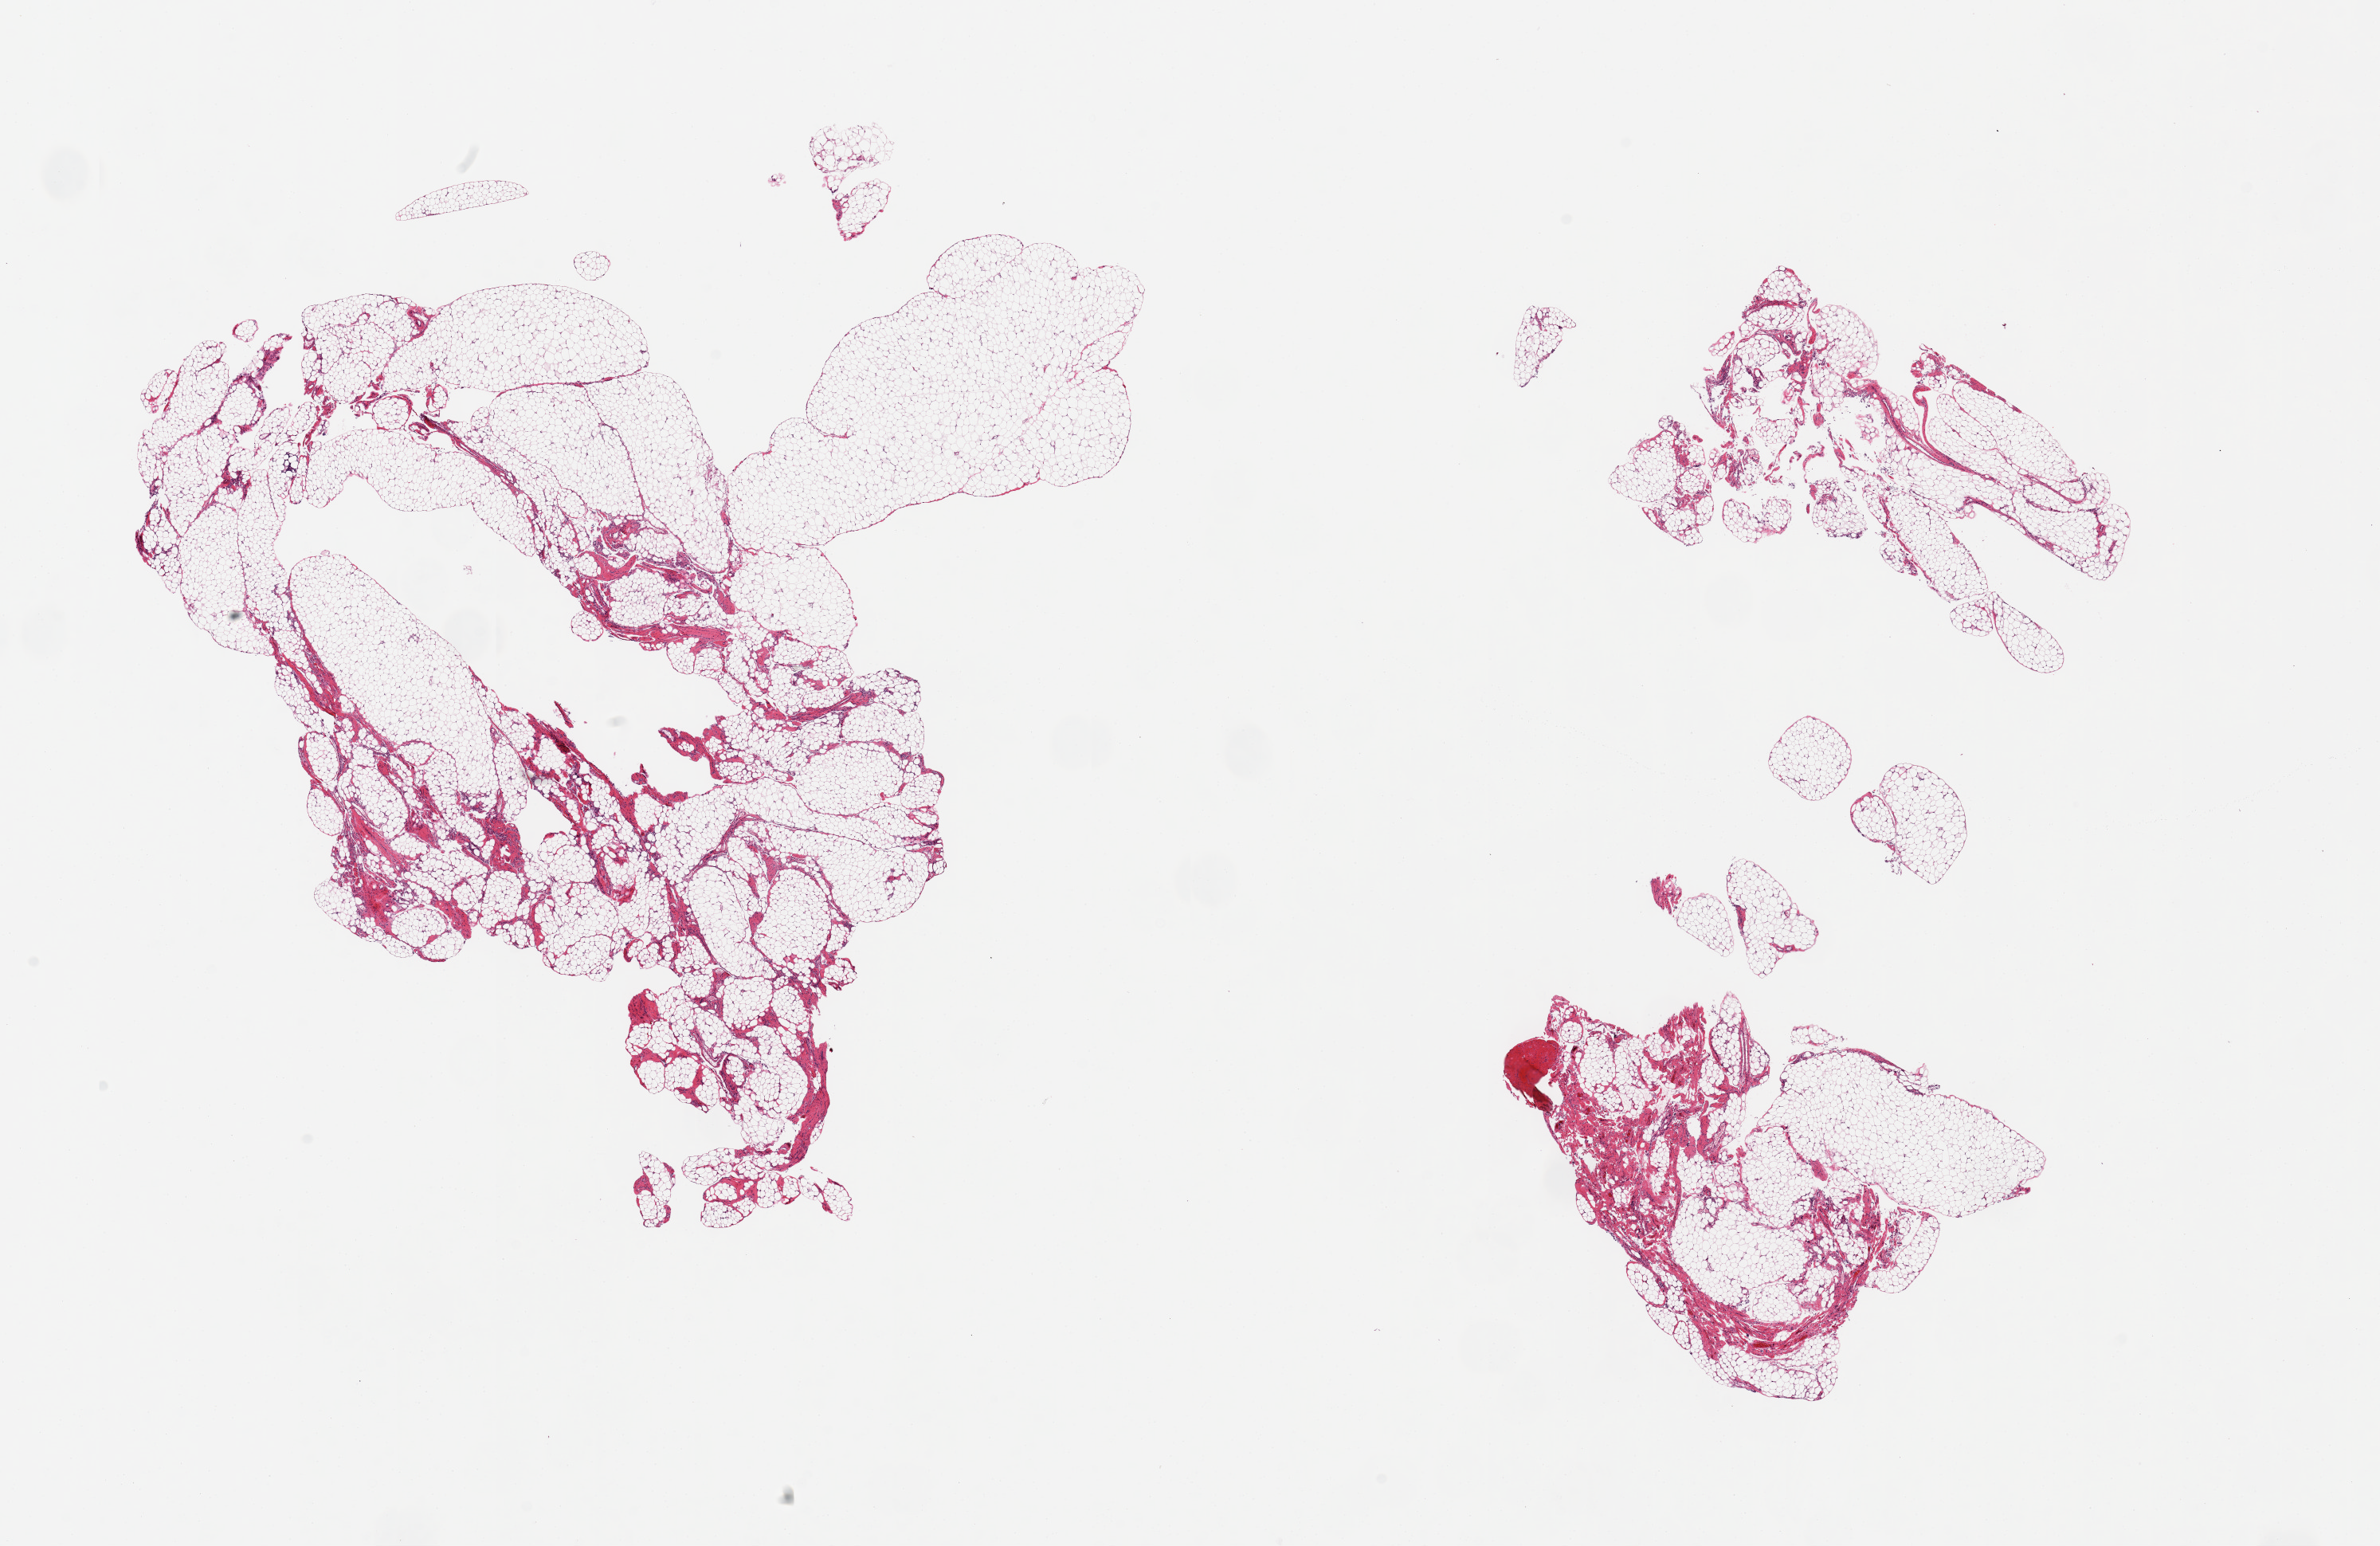
Haematoxylin and eosin whole-slide image — low-resolution overview of the scanned area, about 23.6 x 15.3 mm (slide scanned at 20x); PAXgene-fixed, paraffin-embedded tissue; target tissue: omentum; donor tissue sample. Donor: male.
Review note (as recorded): 2 pieces, prominent fascia/connective tissue, ~30%.